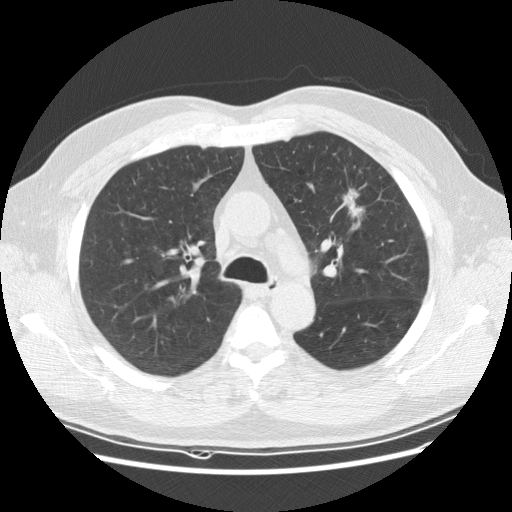
Chest CT (low-dose screening protocol), one axial image; baseline annual screen; lung window (W 1500 / L -600 HU); 2.5 mm slice thickness; slice 47 of 152 in the series. Male participant, aged 65 years at enrolment. Current smoker at enrolment.
Expert reader's lesion annotation, bounding box <322,178,383,234> (left, top, right, bottom; pixels). The screening reader recorded 2 non-calcified nodules or masses ≥4 mm on this exam (left upper lobe, right upper lobe); which of them this box marks is not recorded. Official screen result: positive, change unspecified: nodule(s) >= 4 mm or enlarging nodule(s), mass(es), or other non-specific abnormalities suspicious for lung cancer. Lung cancer was diagnosed 488 days after this screen: carcinoma, NOS, left upper lobe, poorly differentiated (G3), stage IIIA (AJCC 6th edition), 25 mm at pathology.